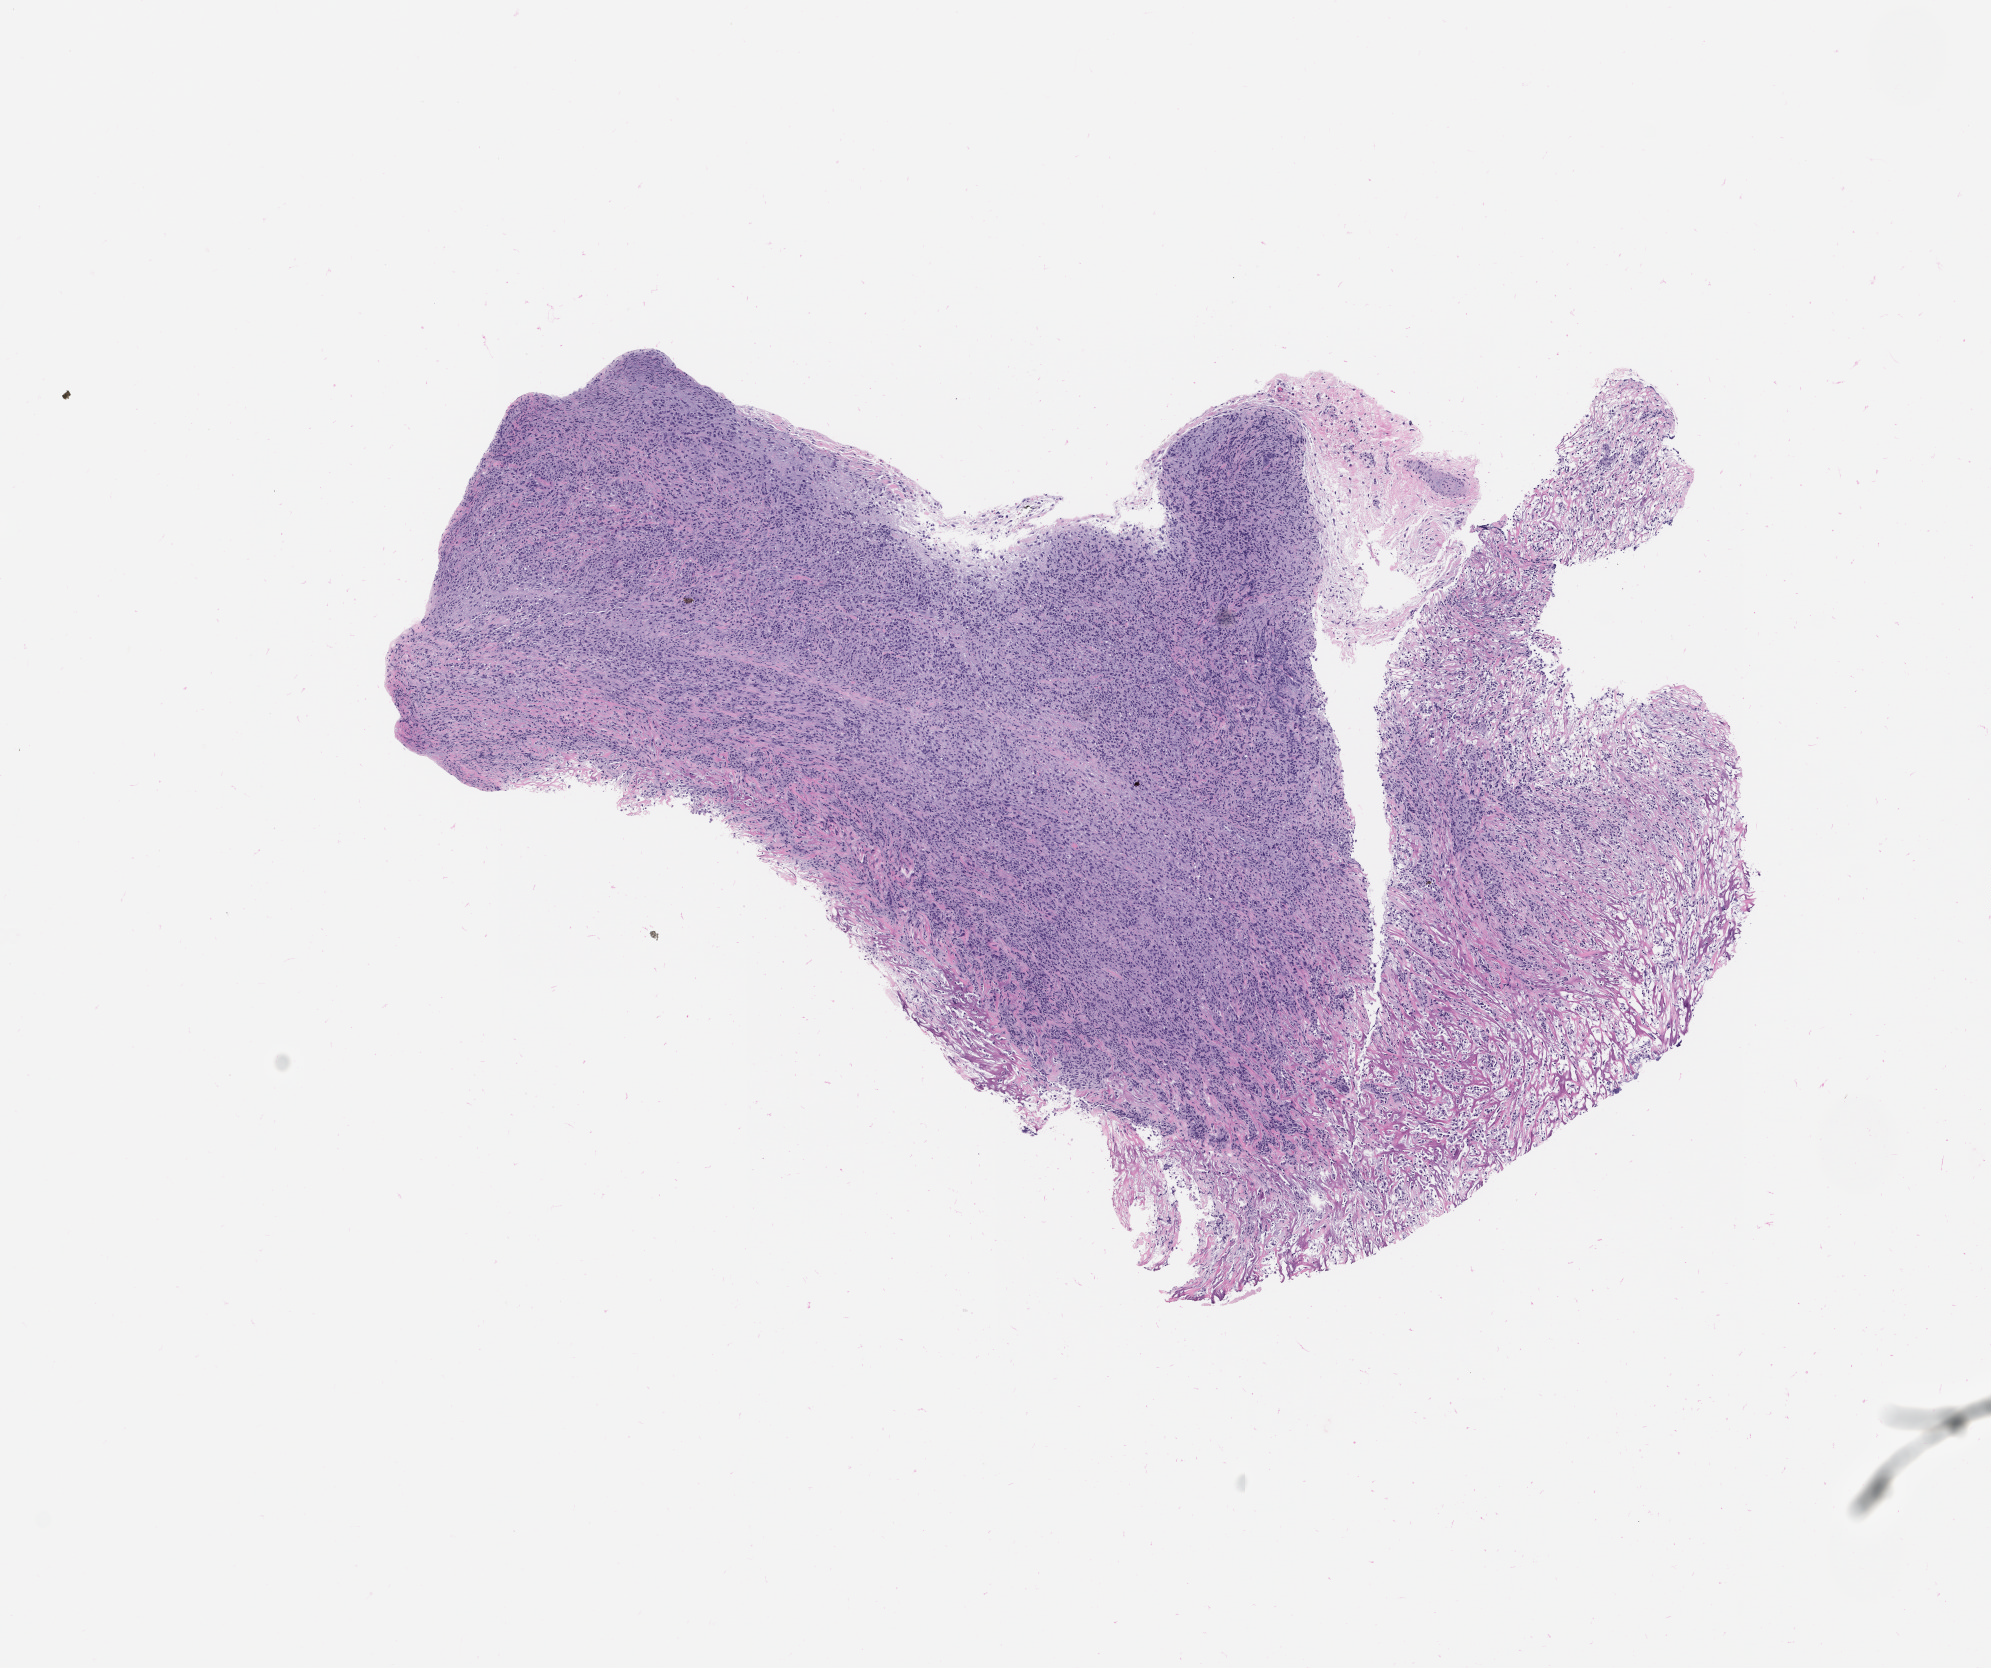
Haematoxylin and eosin whole-slide image of the patient's (originator) tumor tissue, whole scanned area (about 8.0 x 6.7 mm) shown as a low-resolution overview; formalin-fixed paraffin-embedded section; originating tumor site category: bone. Patient male; age 72 years.
Diagnosis: Osteosarcoma.